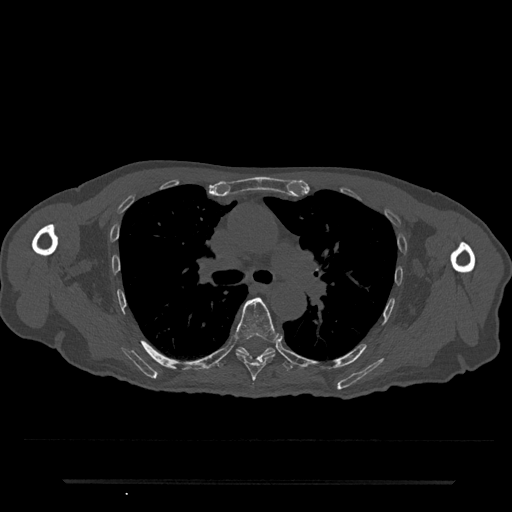
CT including the spine, one axial slice. Position 516 of 797 along the scan axis. 120 kVp. Bone window (W 1800 / L 400 HU). 0.5 mm slice thickness. 512 × 512 image matrix, field of view 427 × 427 mm. Male patient, age 74 years. Case-level facts recorded for this patient, not image findings: primary cancer: prostate.
Structures marked on this image (semi-automatic segmentation, software-assisted and operator-edited):
- T6 vertebra: bounding box (x1, y1, x2, y2) in pixels: (234, 297, 279, 382)
- T7 vertebra: (217, 347, 293, 370)